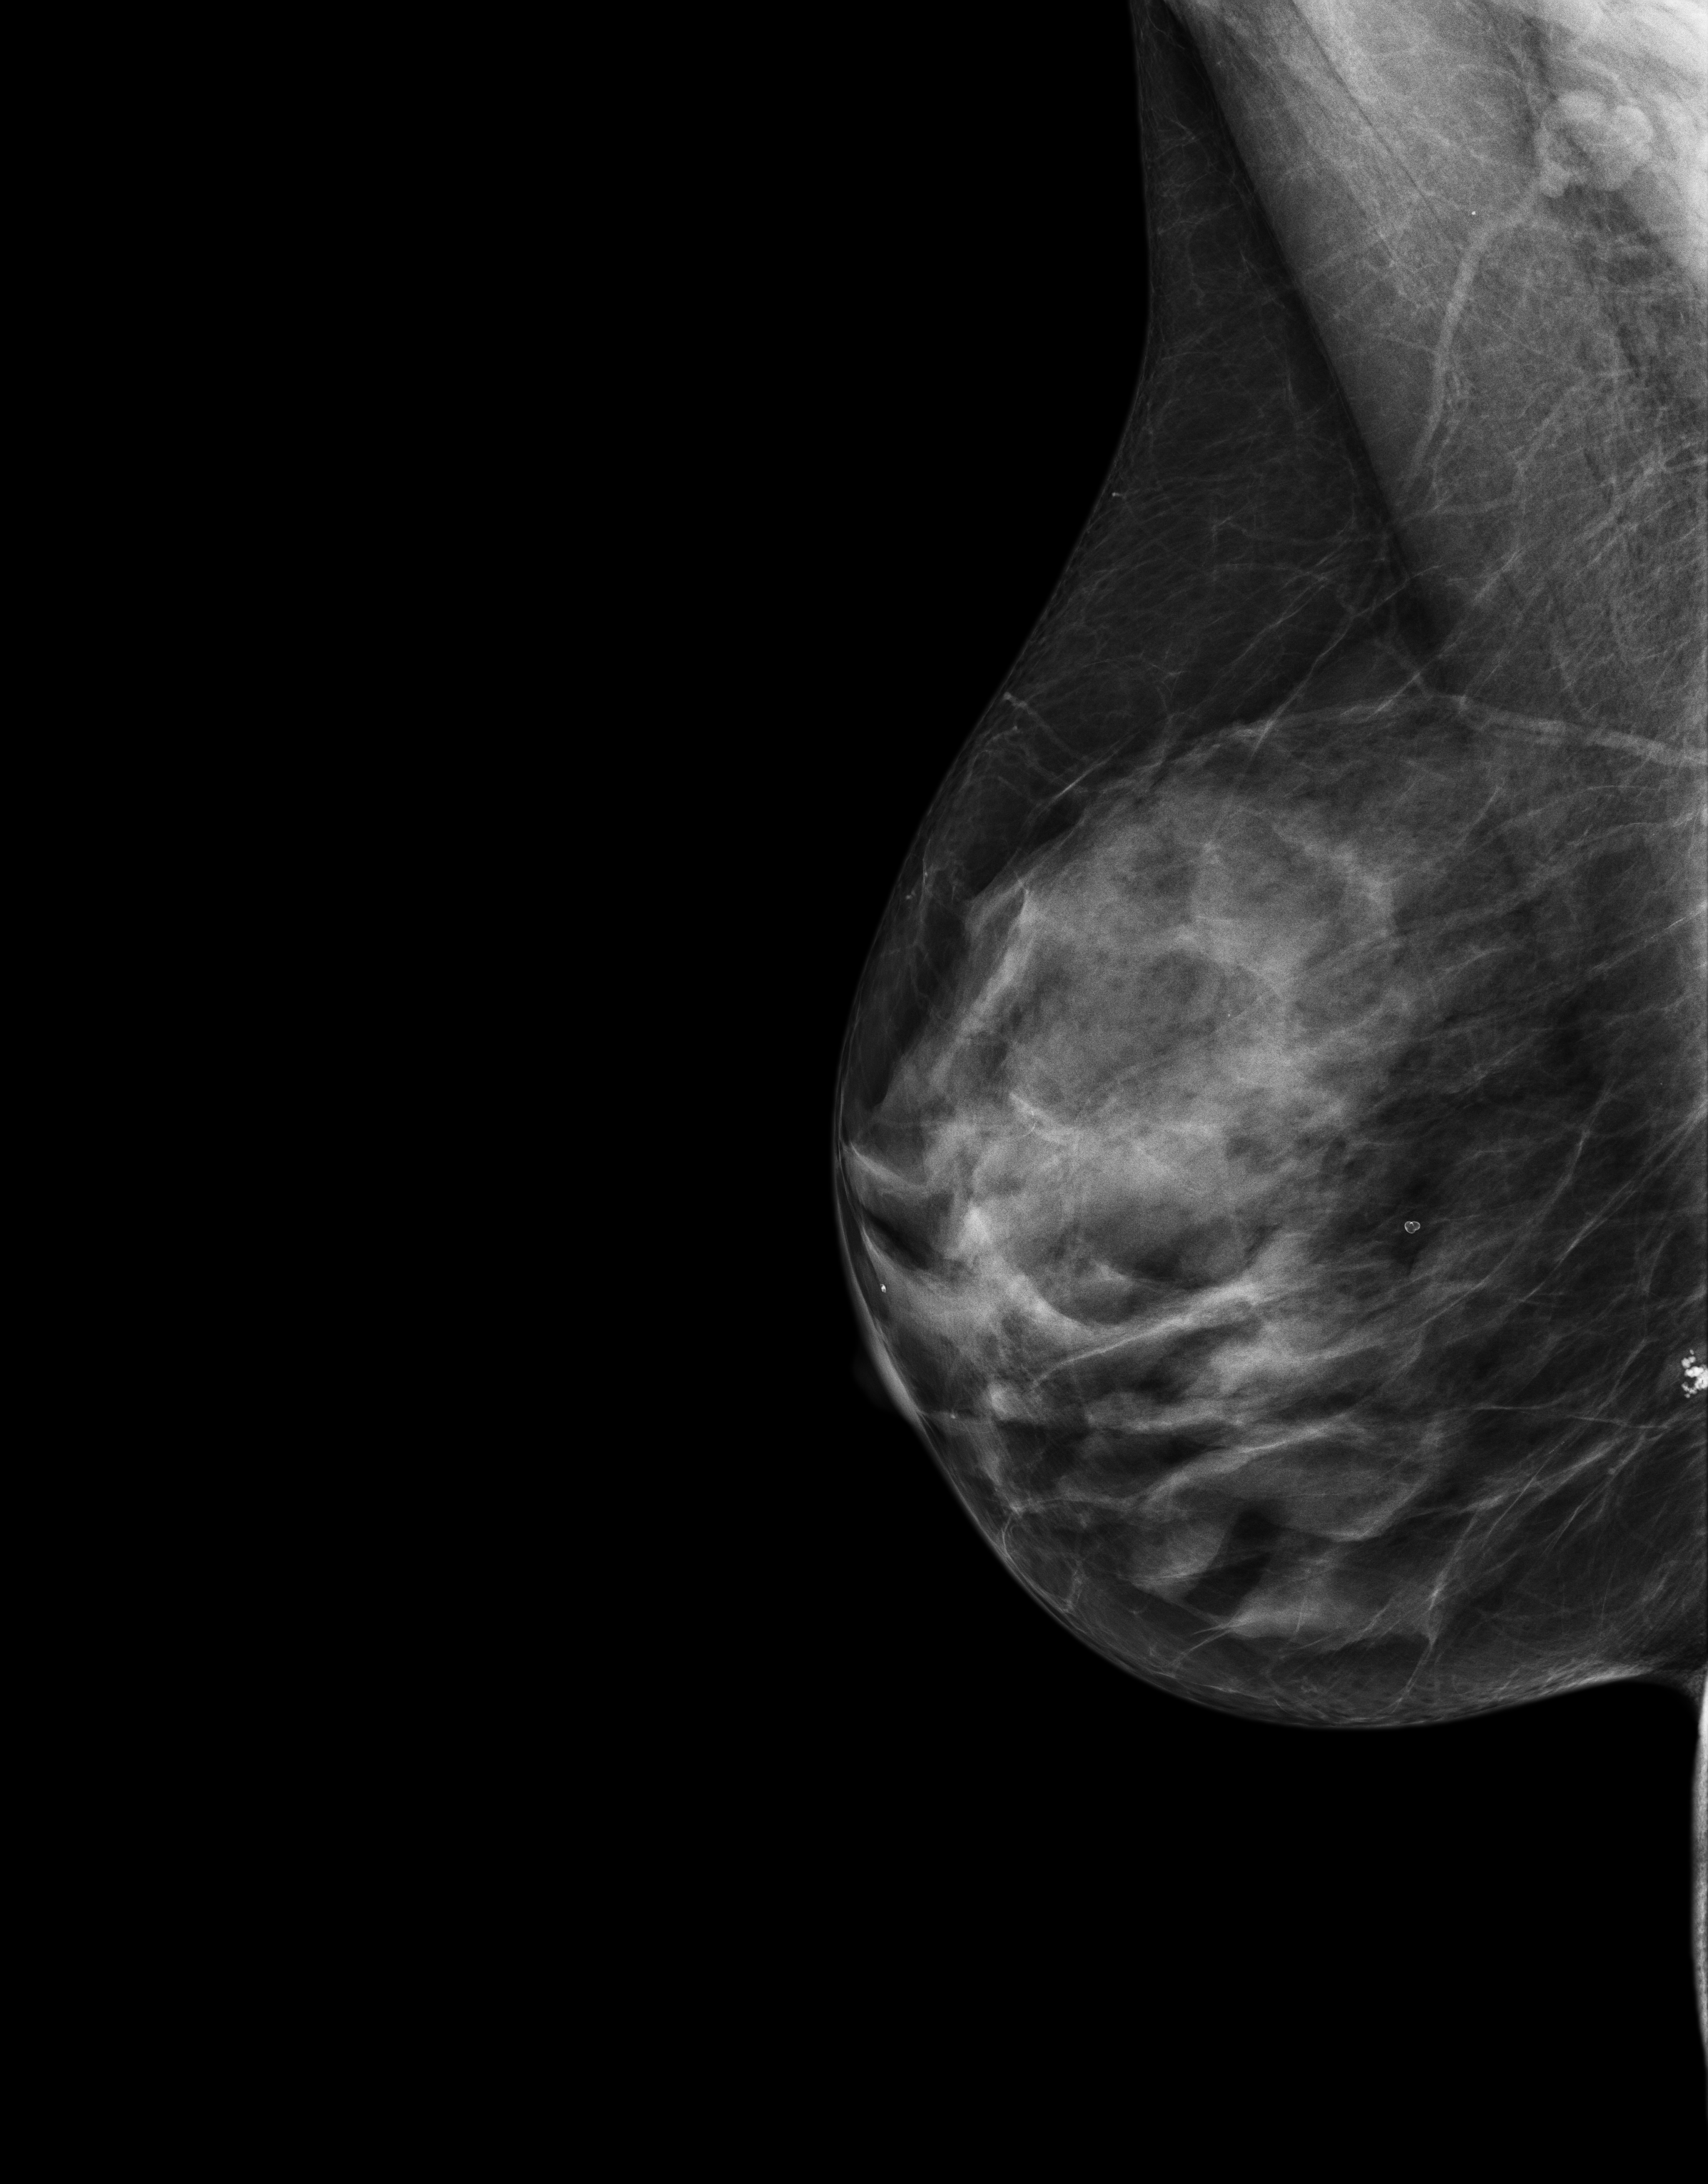
Screening examination; system: Senographe Essential ADS_56.21.3. Patient aged 61 years (female).
Image type: full-field digital mammogram. Breast: right. Projection: MLO view.